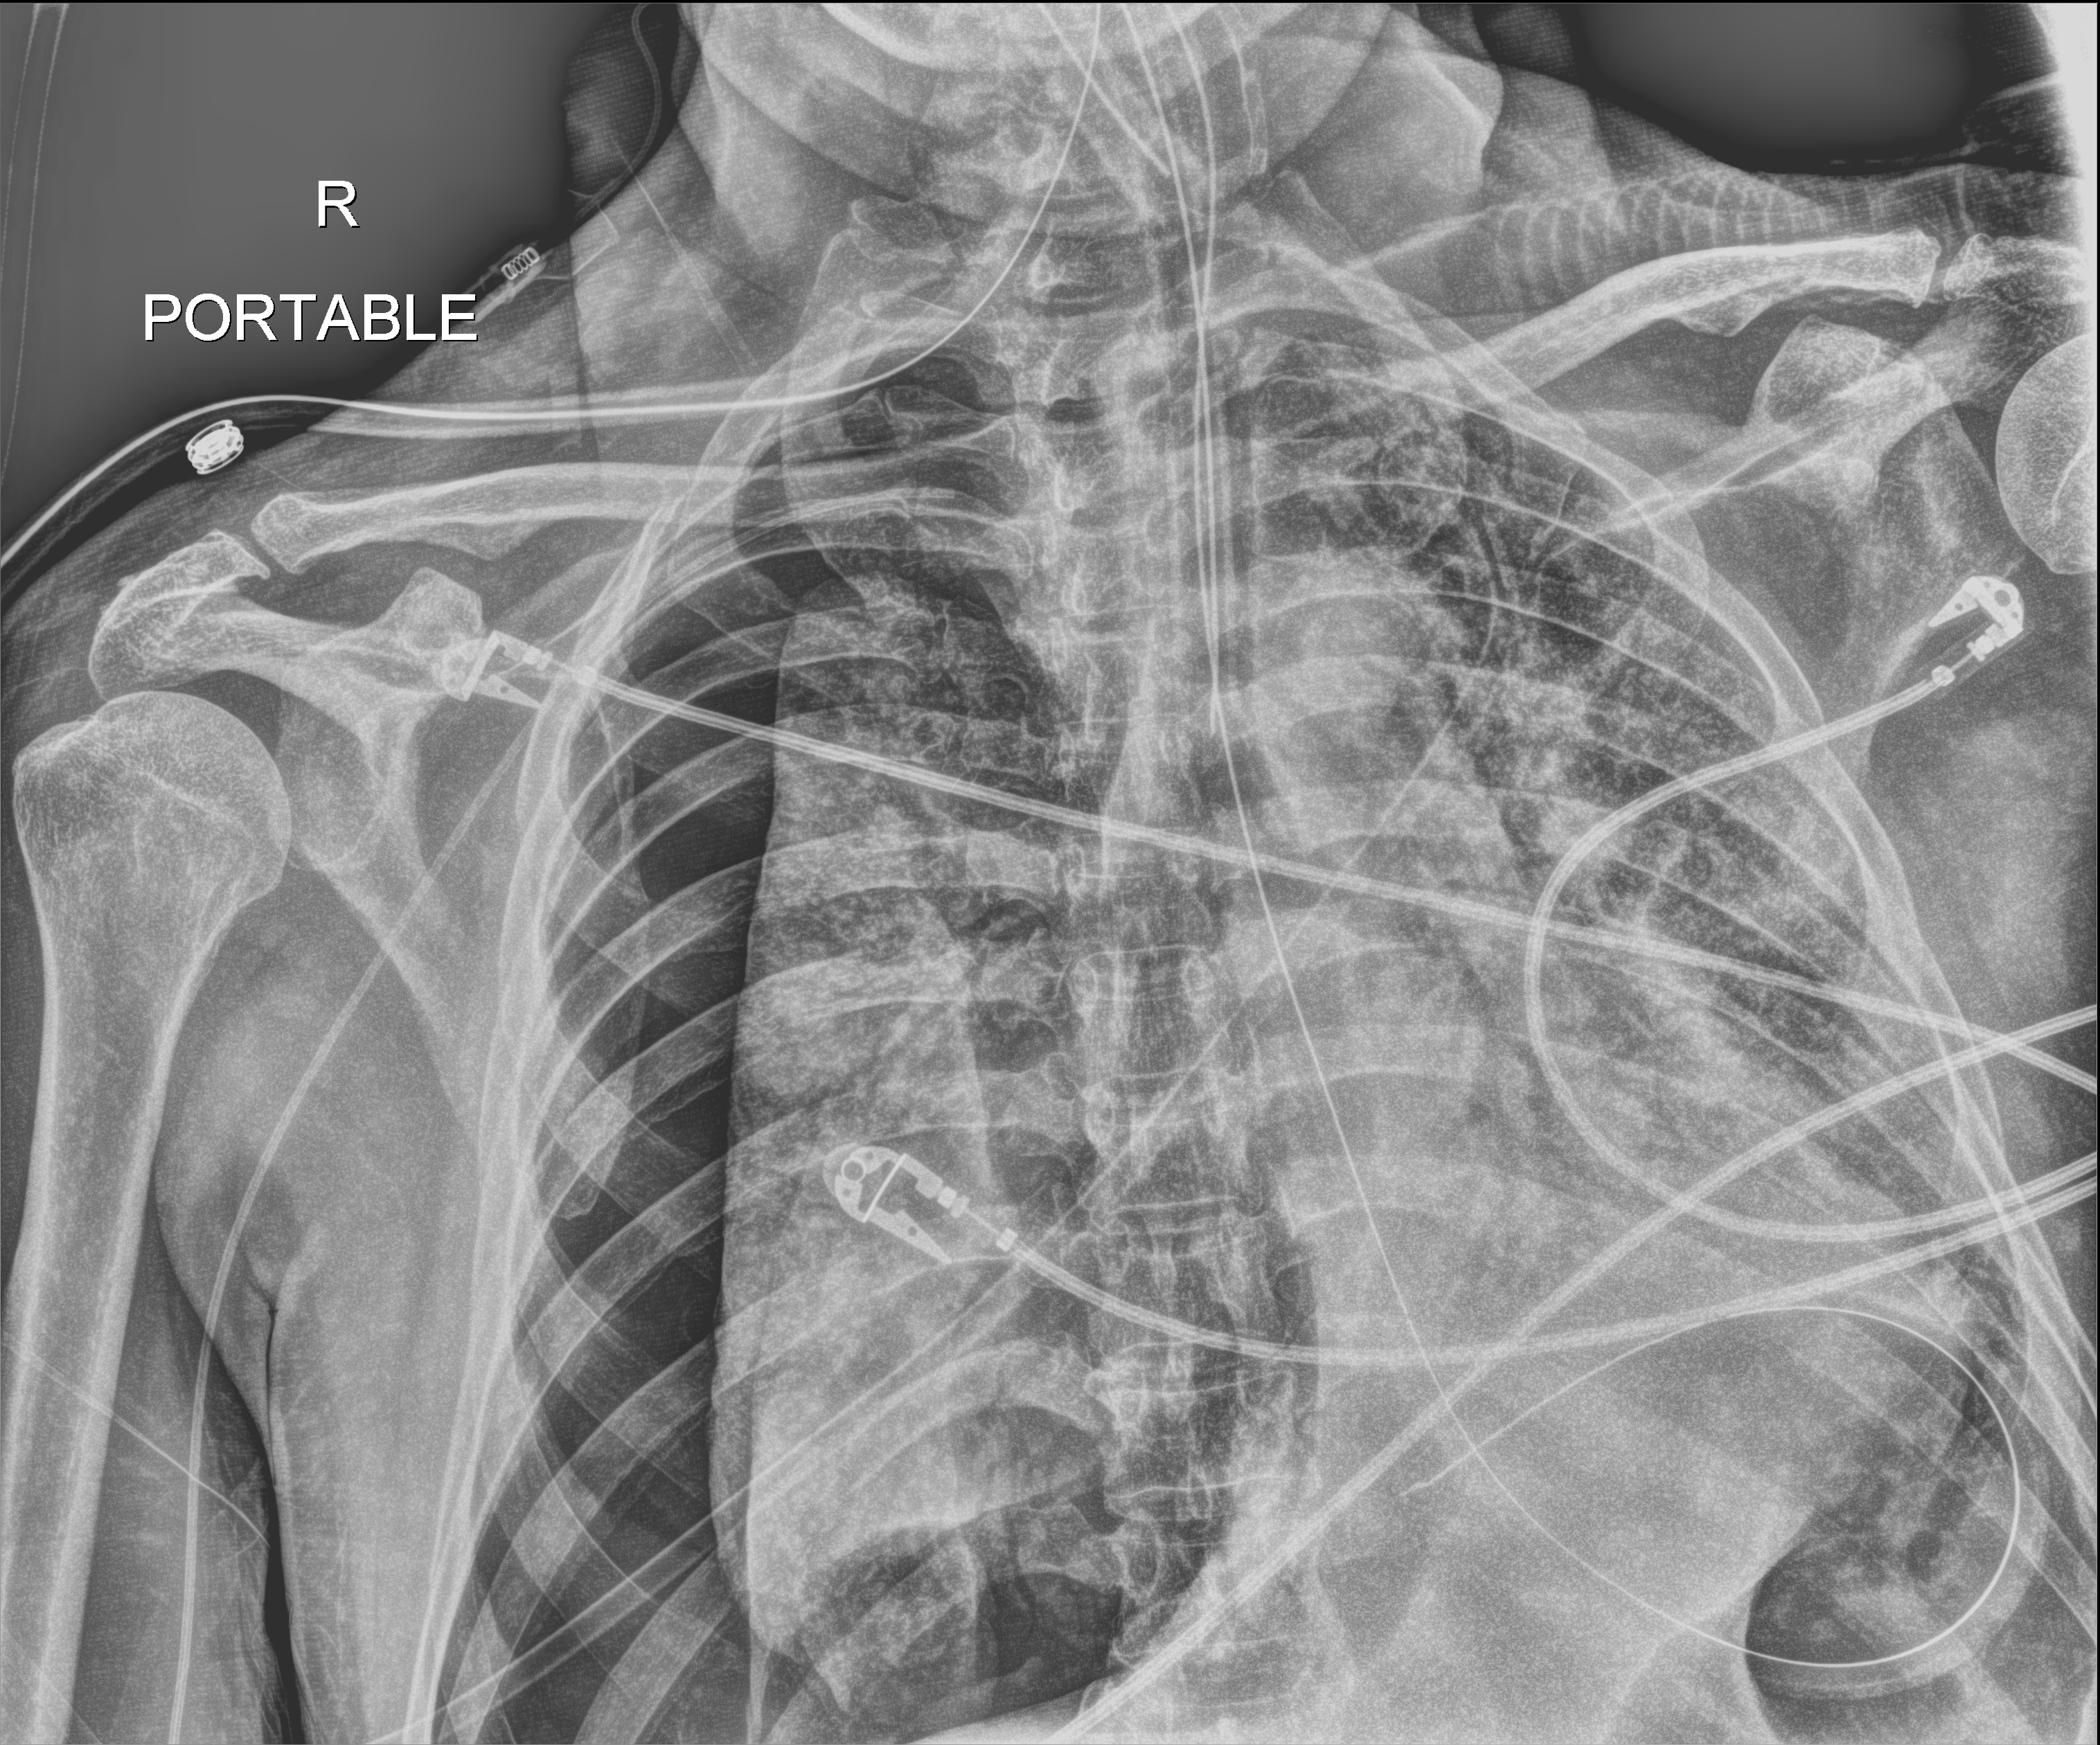
Chest radiograph. Male patient hospitalised with COVID-19, age 60–74 years.
Admission-level facts for this patient (not findings on this image; timing relative to this image not recorded):
- length of hospital stay: 37 days
- mechanically ventilated during this hospital stay: yes